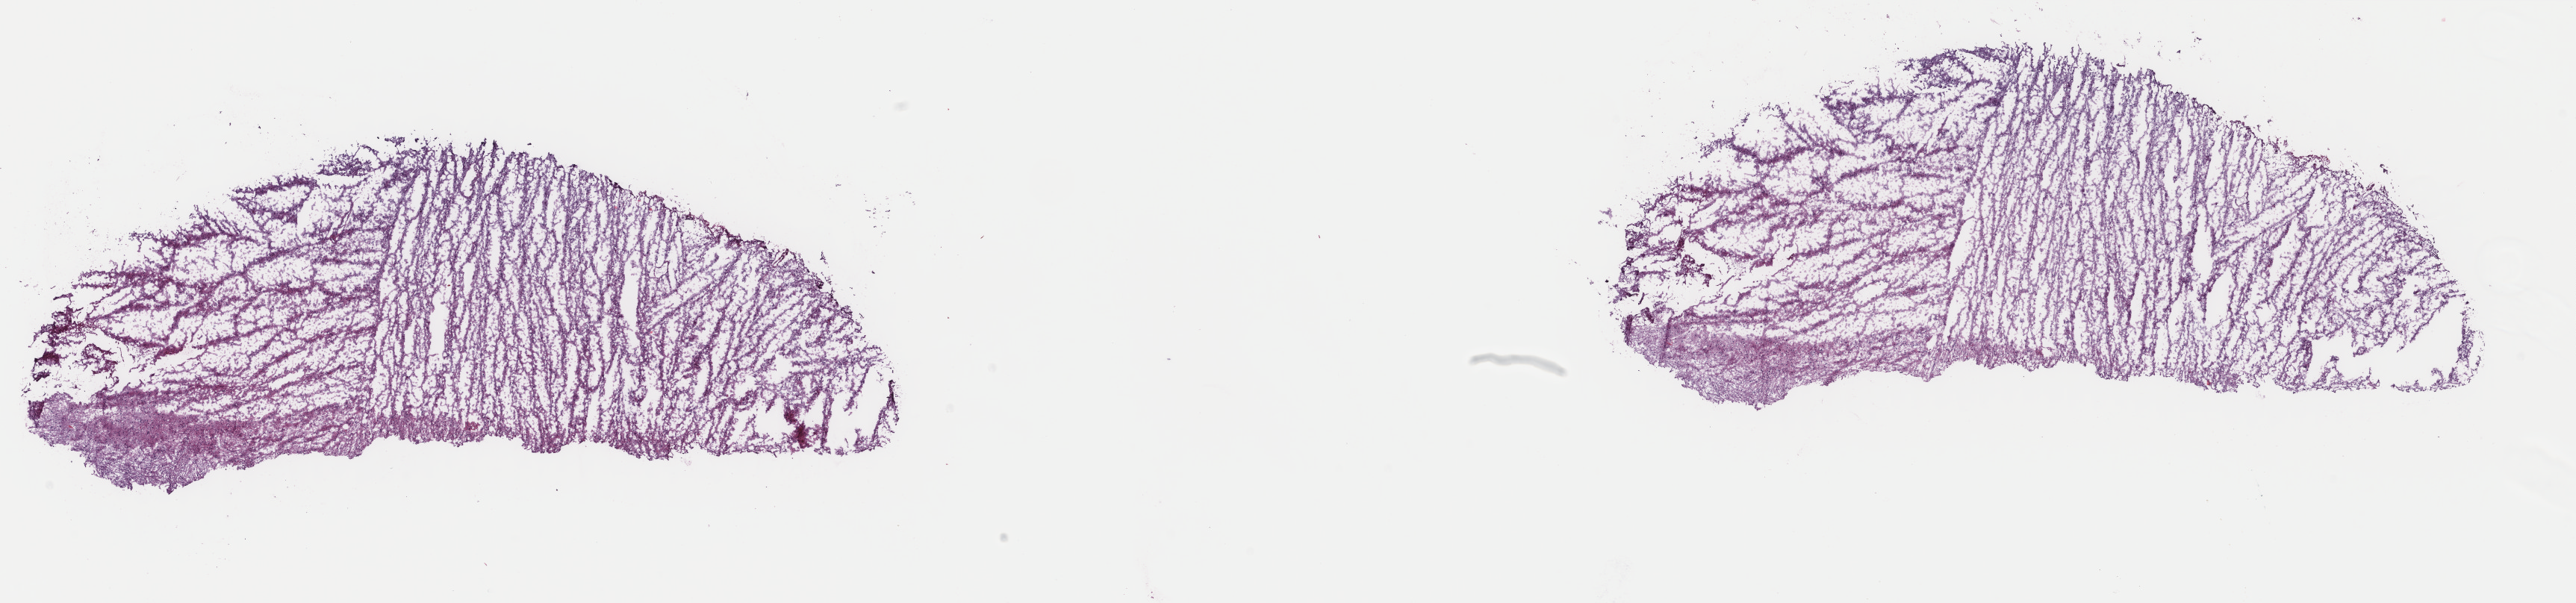
Digitized H&E tissue section (whole slide) — low-resolution overview of the scanned area, about 27.4 x 6.4 mm (from a 40x scan). Frozen section from the top of the tissue portion. Primary tumour sample from the brain. Female, age 44 years at initial diagnosis. Histologic grade: G3 (poorly differentiated). Slide review estimates, as recorded: tumour cells 45%, tumour nuclei 75%, normal cells 10%, stromal cells 45%, necrosis 0%. Inflammatory infiltration, as recorded: lymphocyte infiltration 0%, monocyte infiltration 0%, neutrophil infiltration 0%.
Laterality: right. Diagnosis: Astrocytoma, anaplastic.